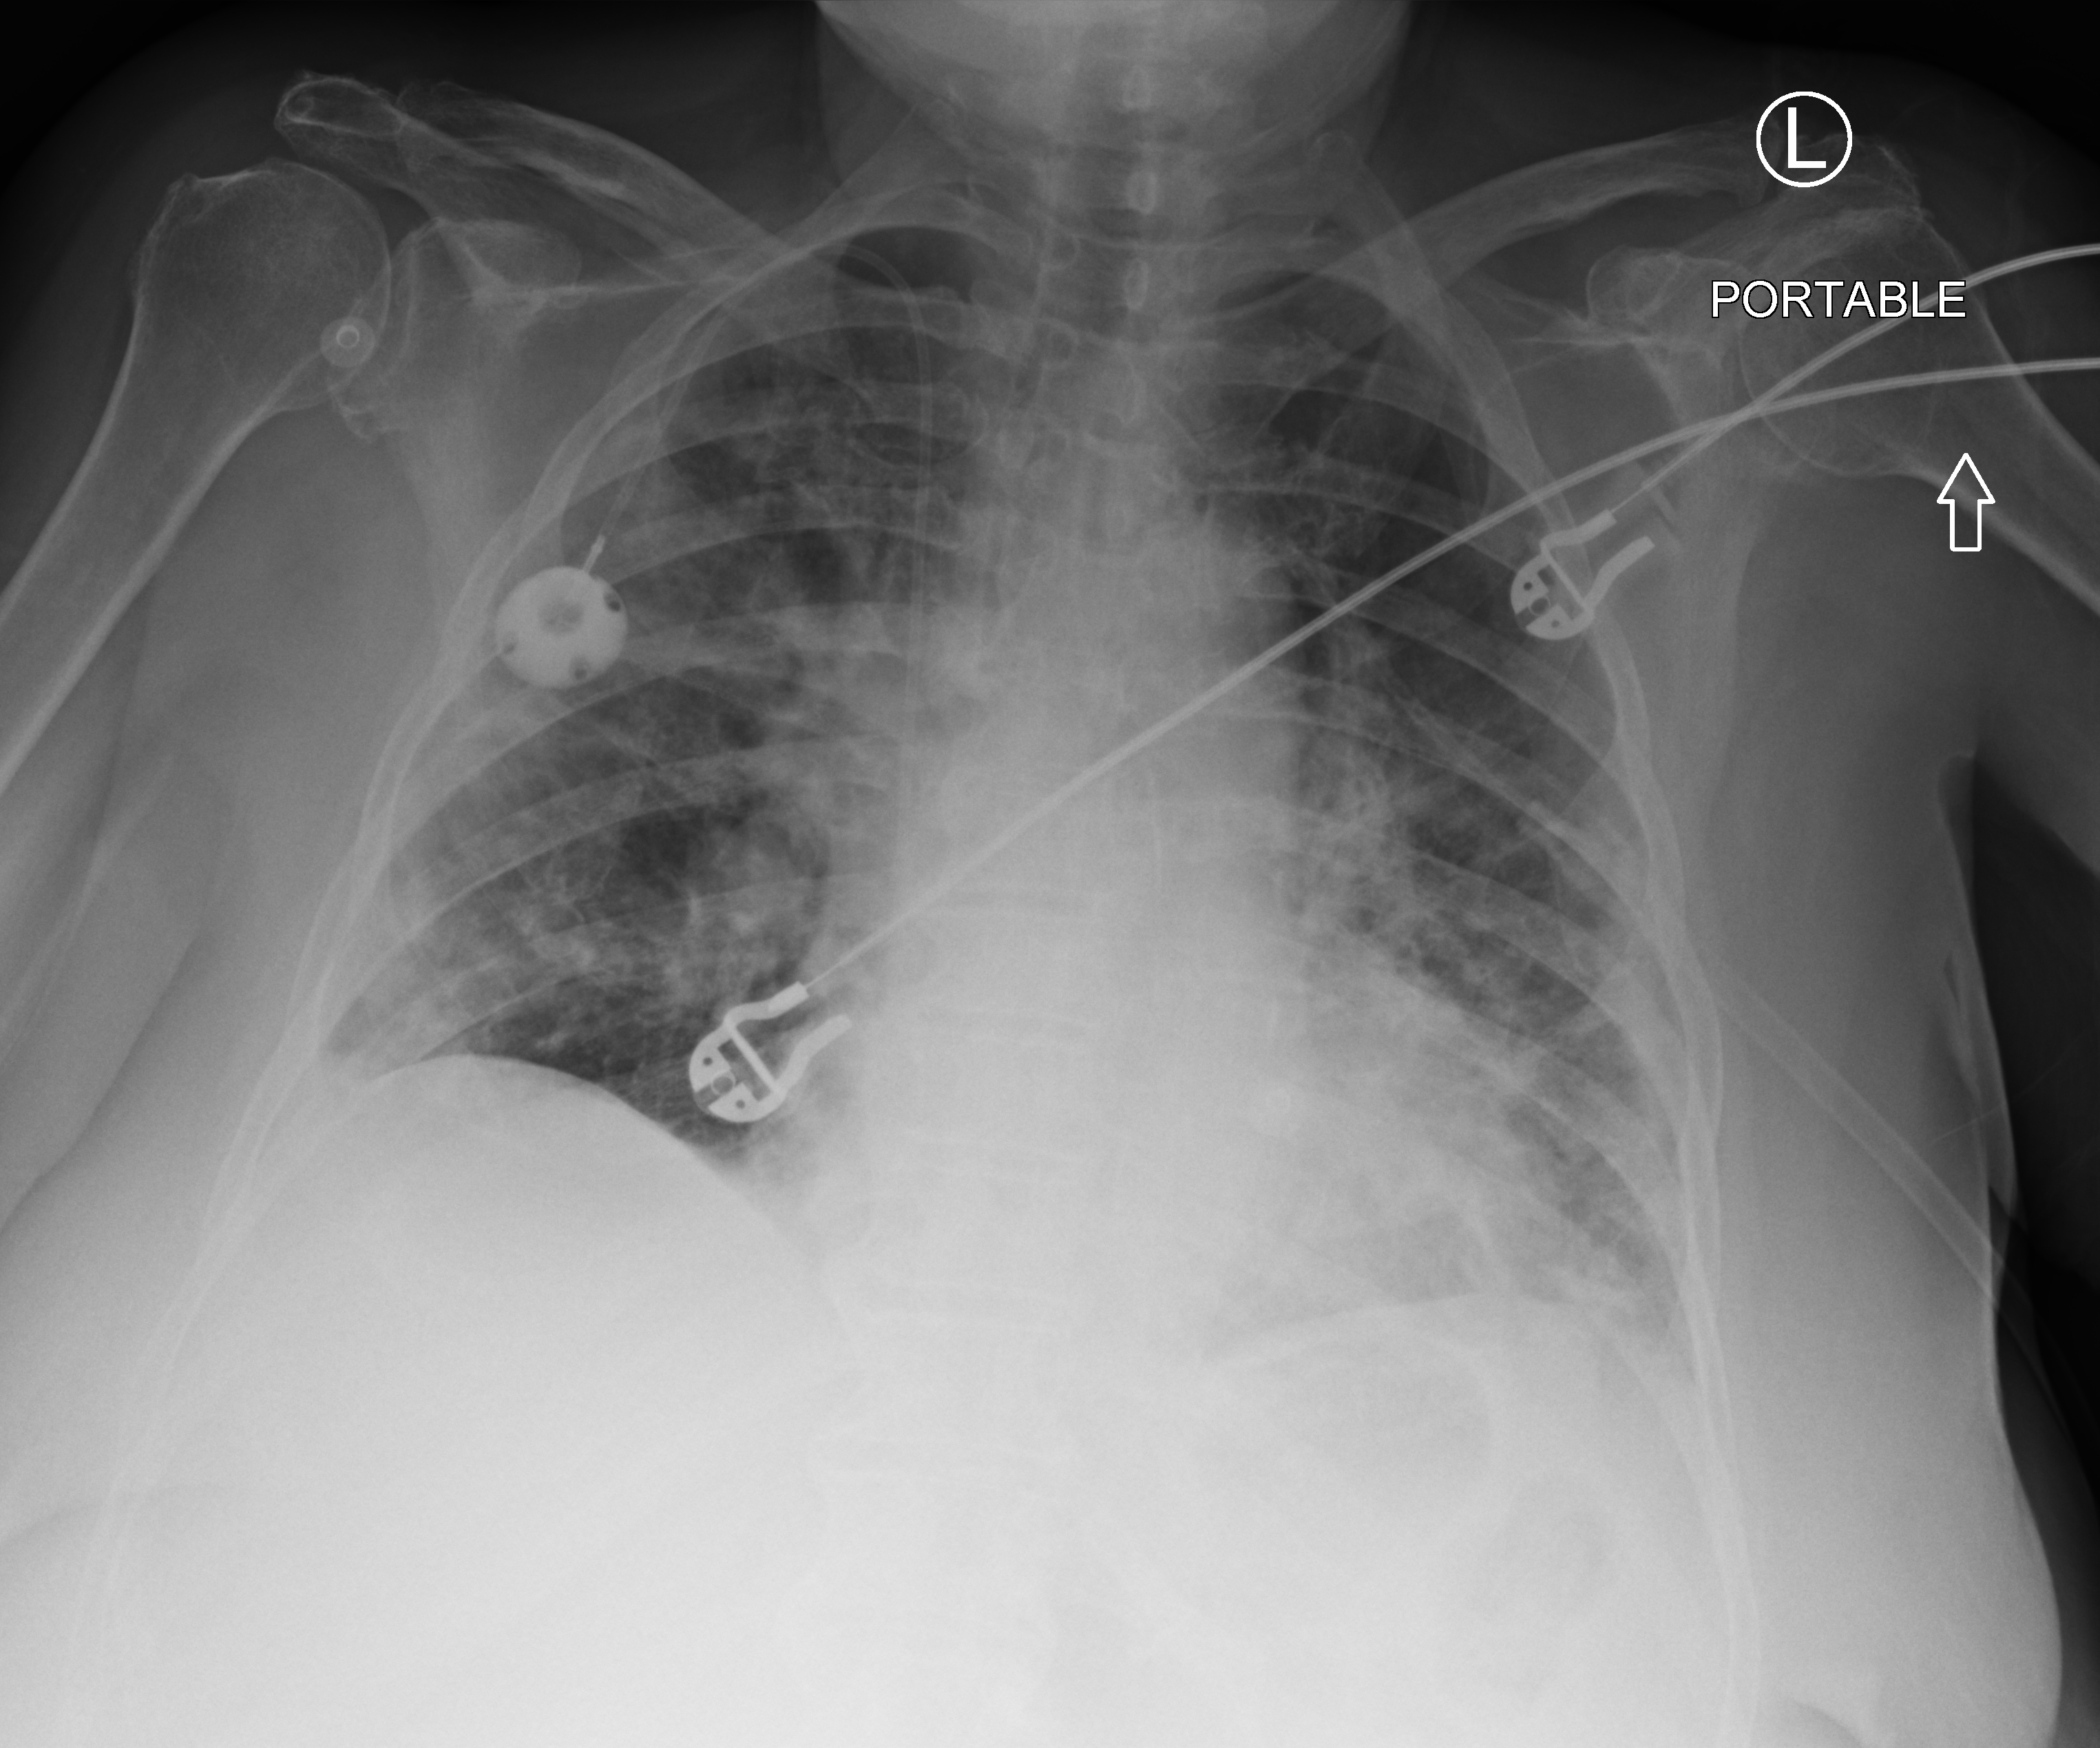
Bedside chest radiograph (computed radiography). Female patient hospitalised with COVID-19, age 75–90 years.
Hospital-stay facts (about this admission, not read from this image; timing relative to this image not recorded): admitted to intensive care during this hospital stay: no; length of hospital stay: 13 days; mechanically ventilated during this hospital stay: no.